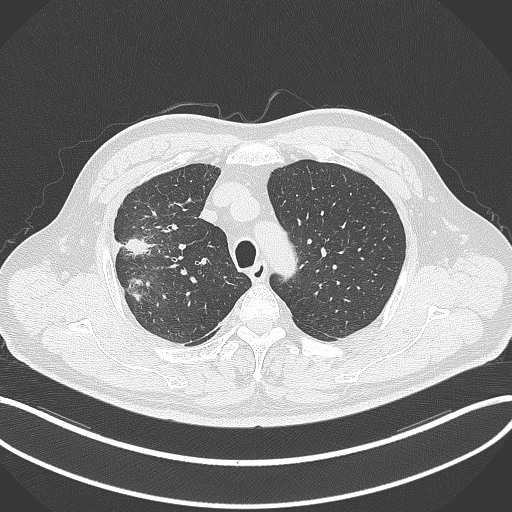
Chest CT, one axial slice; position 267 of 348 along the scan axis; lung window (W 1500 / L -600 HU); 1 mm slice thickness; 512 × 512 image matrix. Patient: male, 55 years. From the clinical record (not read from this slice): clinical TNM (as recorded): T3 N2 M1.
Annotated regions visible in this slice (rectangle marked by the reading radiologist):
- lung tumour (recorded histology: adenocarcinoma): bounding box <120,237,155,302> (left, top, right, bottom; pixels)